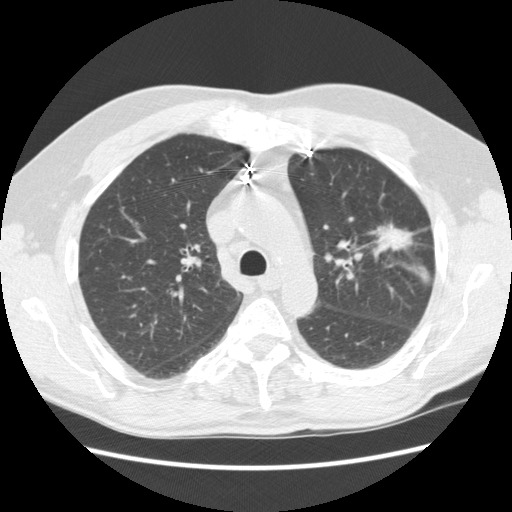
Chest CT (low-dose screening protocol), one axial image, baseline screening round, lung window (W 1500 / L -600 HU), 2.5 mm slice thickness, slice 168 of 231 in the series. Male, age 72 years at enrolment. Former smoker at enrolment.
• Expert reader's lesion annotation, bounding box [x1, y1, x2, y2] px = [359, 210, 428, 260].
• Reader record for this screening exam (exam-level; its link to the box is not recorded): non-calcified nodule or mass ≥4 mm, left upper lobe, 25 × 18 mm, spiculated (stellate) margins, soft tissue attenuation.
• Later outcome: lung cancer diagnosed 35 days after this screen — adenocarcinoma, NOS, left upper lobe, well differentiated (G1), stage IIIB (AJCC 6th edition), 25 mm at pathology.